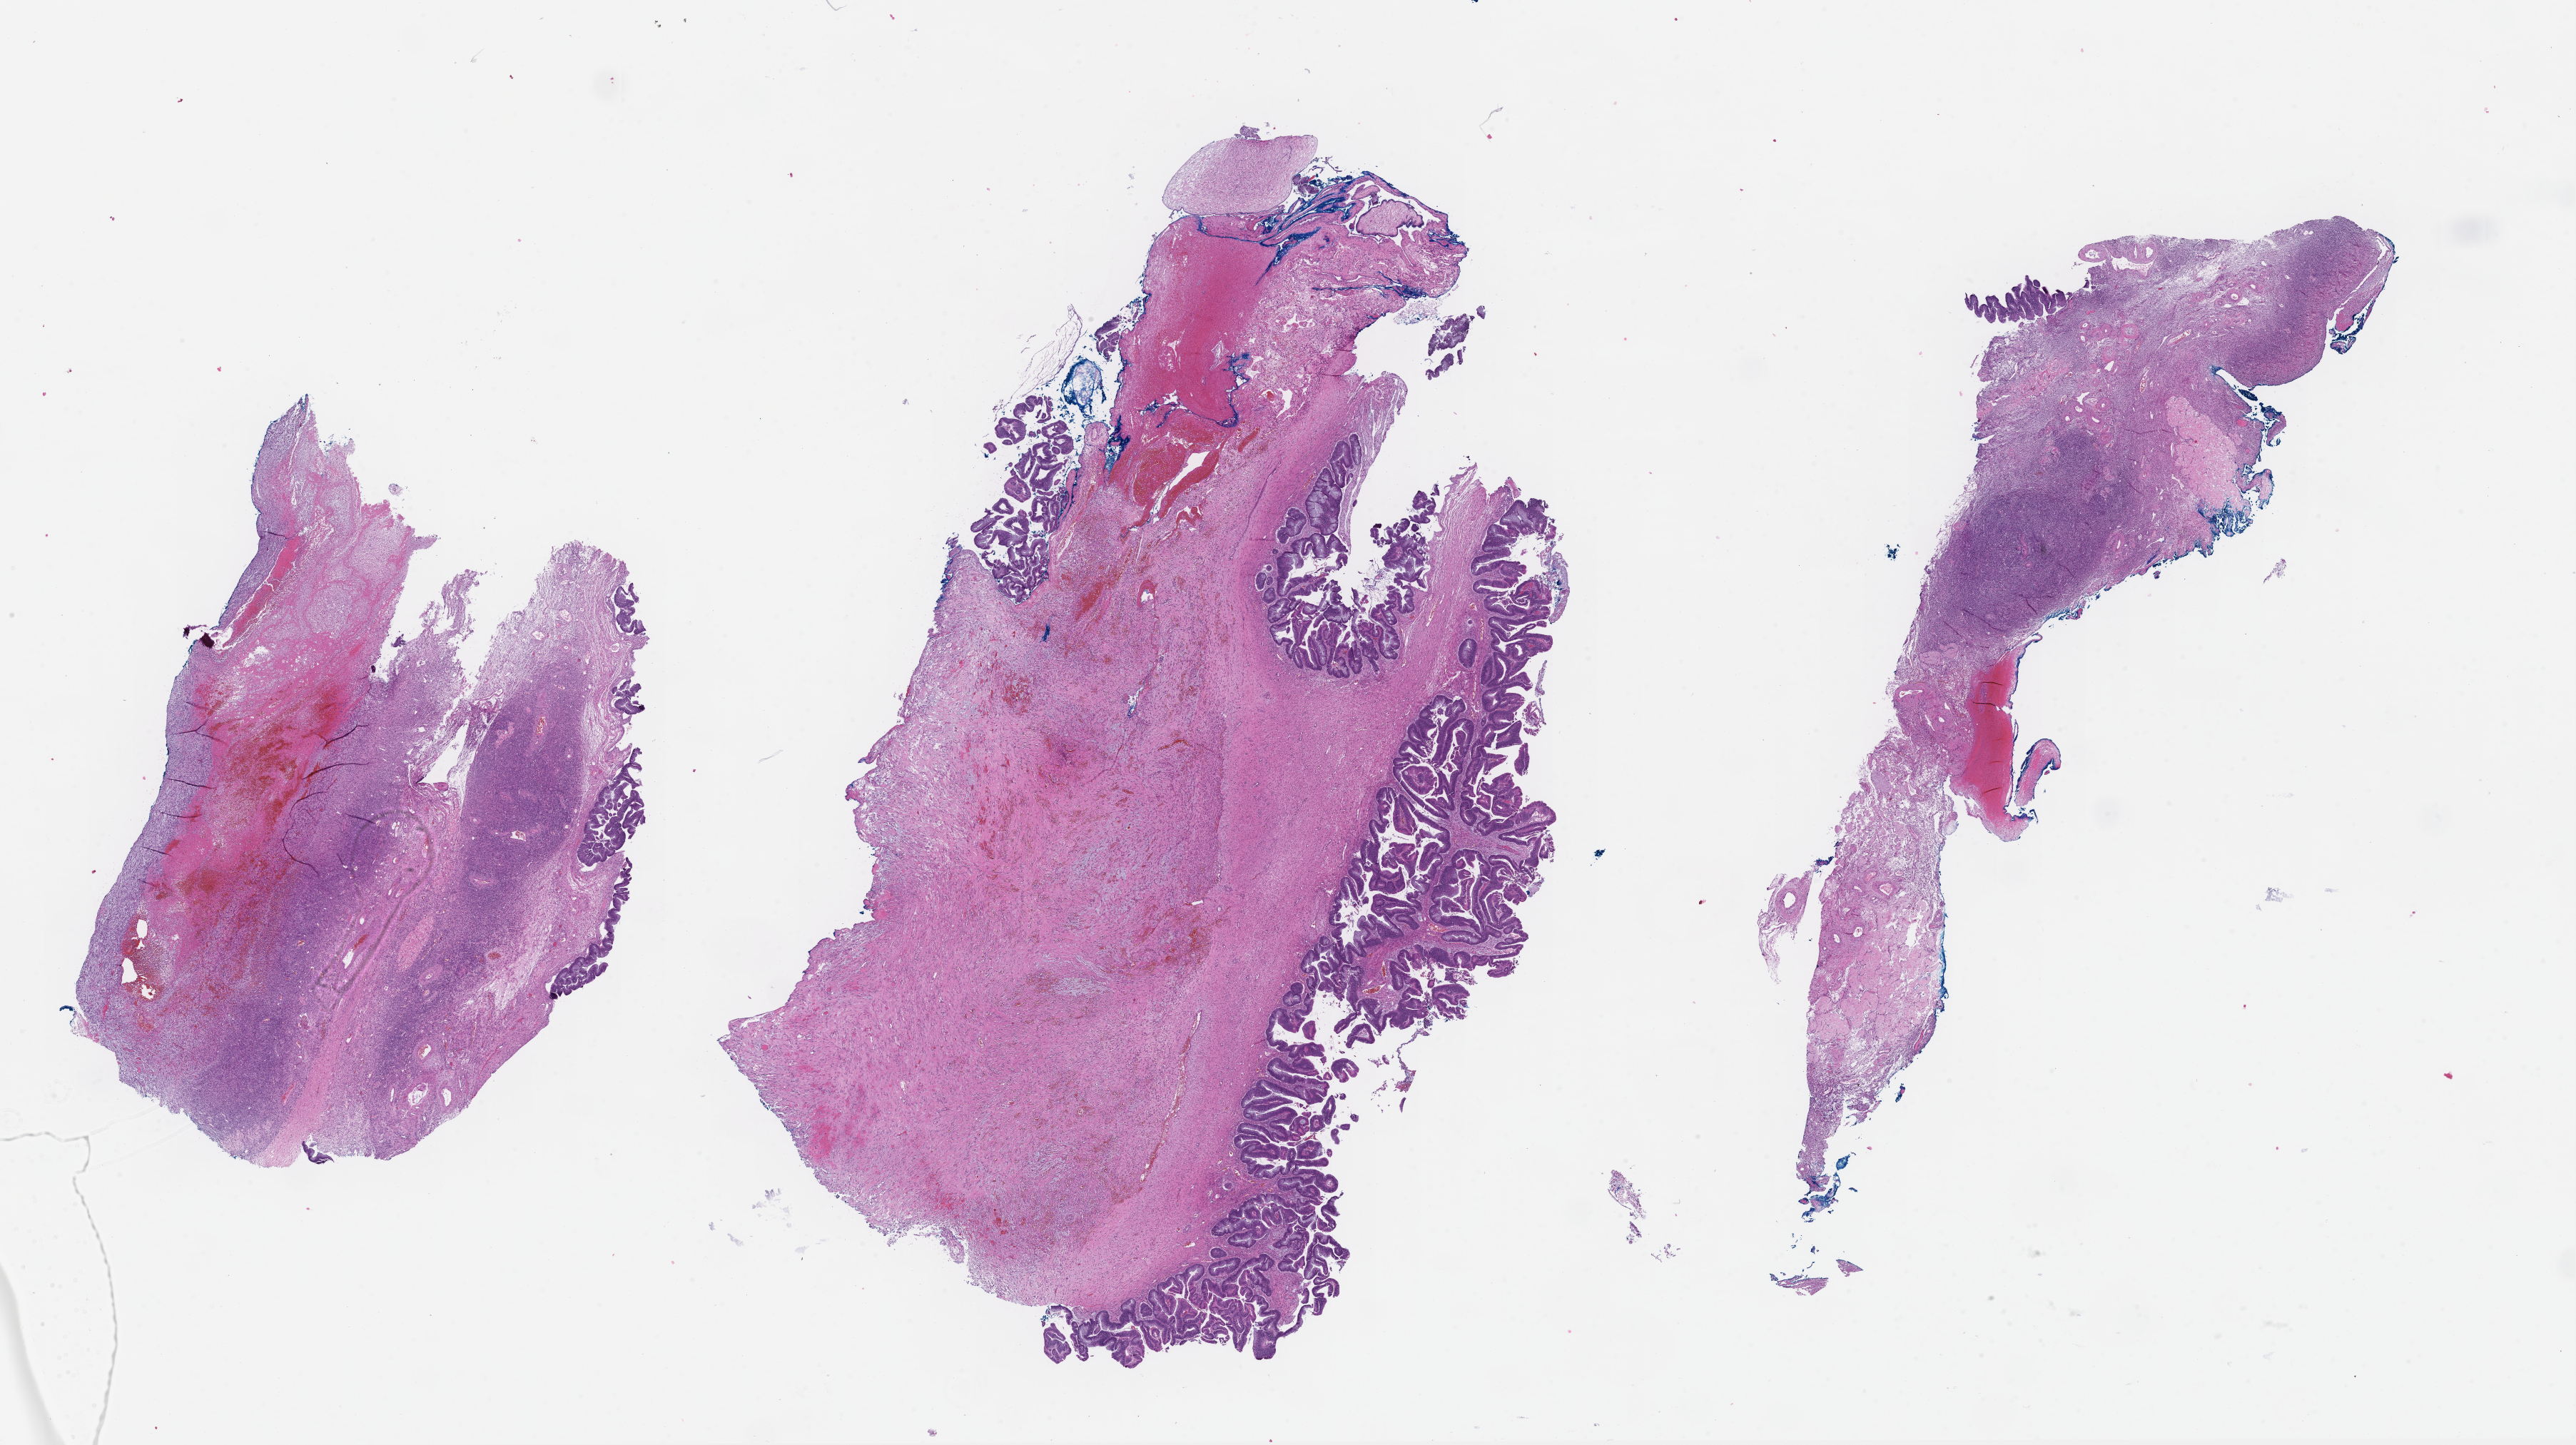
Whole-slide image, H&E stain, shown as a low-resolution overview of the whole scanned area (about 29.1 x 16.4 mm), FFPE section, specimen time point: archival tissue. Patient: female.
• this section: metastasis (sampled organ not recorded)
• patient diagnosis (primary): Colorectal Carcinoma